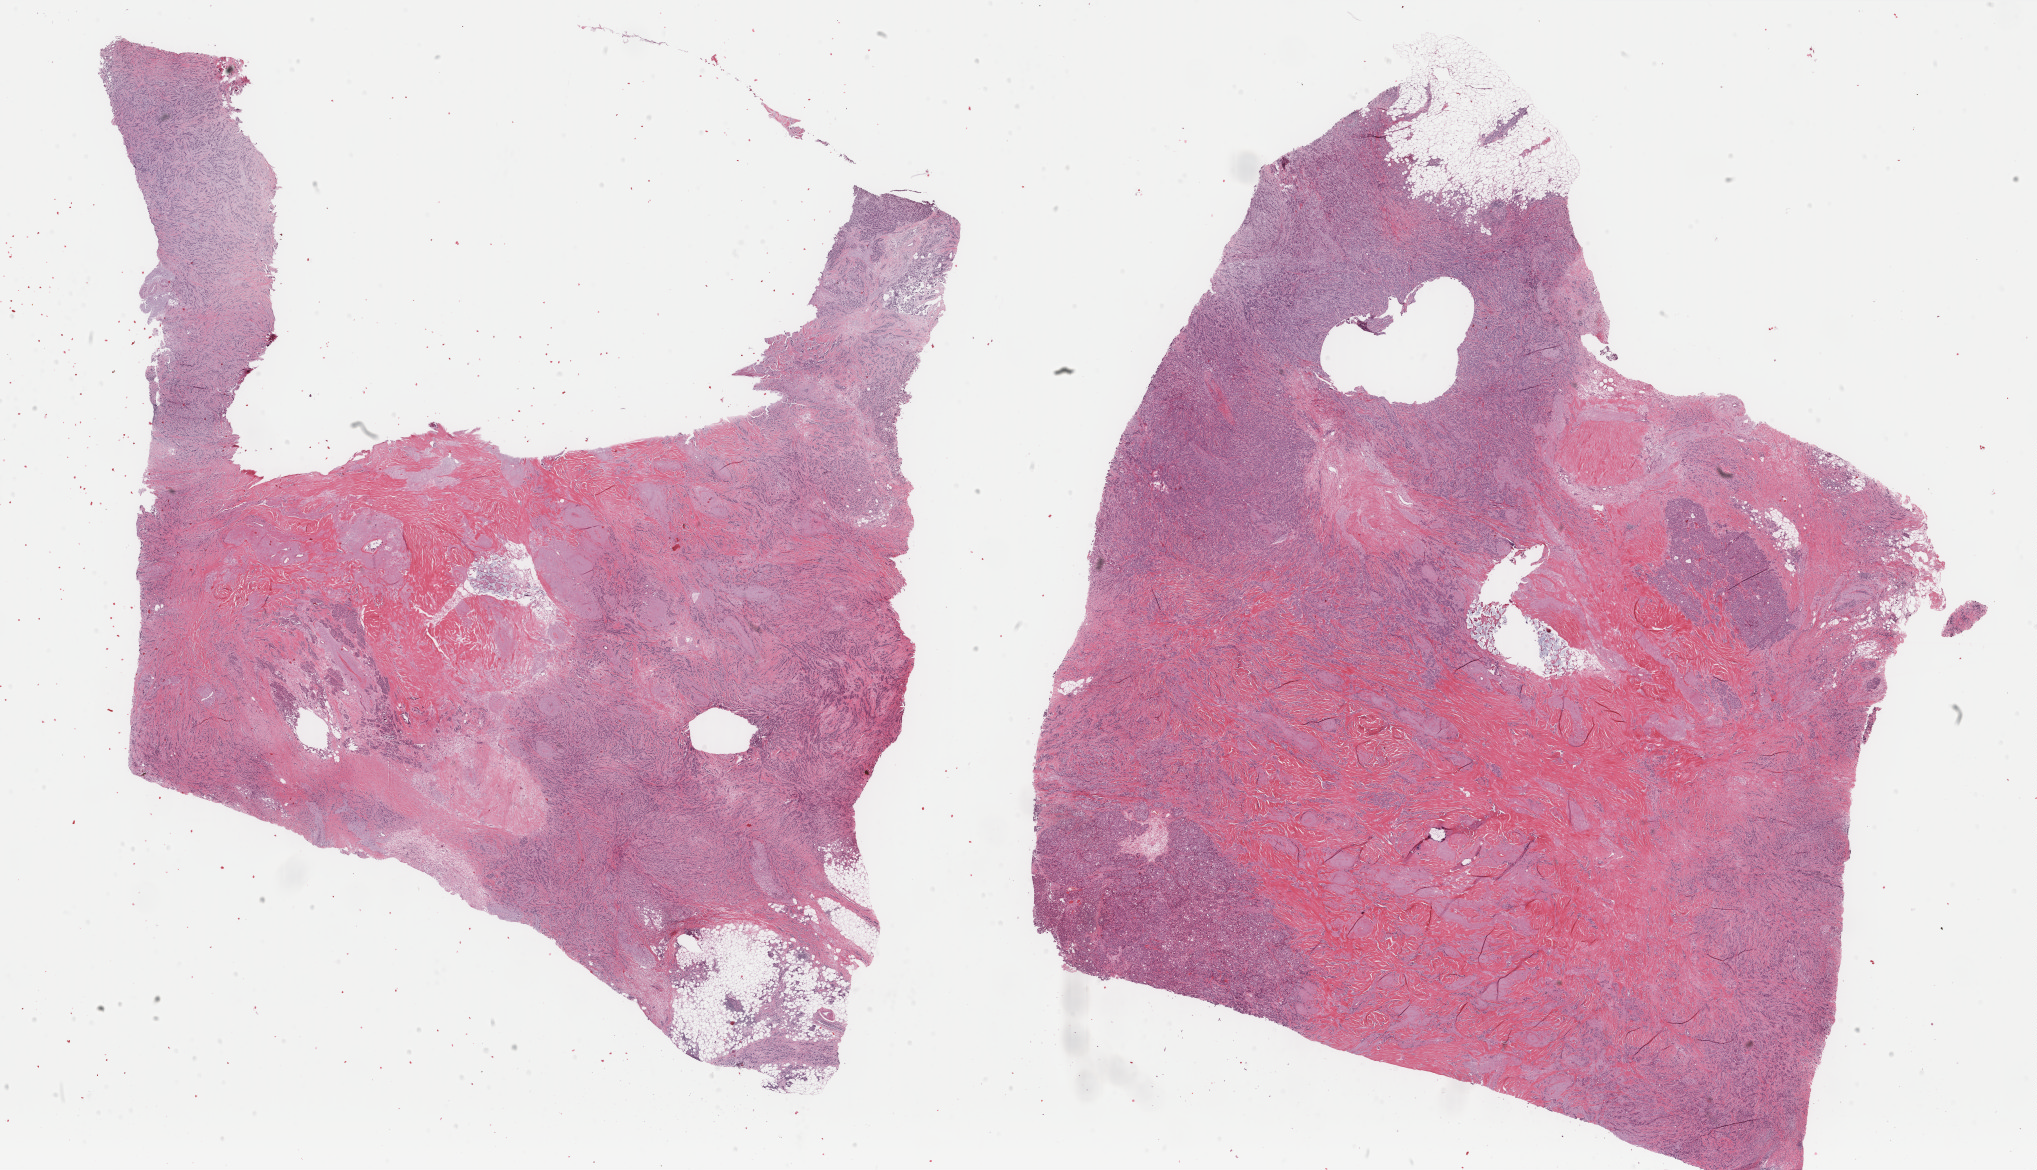
Hematoxylin and eosin (H&E) stained whole-slide image, shown as a low-resolution overview of the whole scanned area (about 32.3 x 18.6 mm), FFPE section, breast, primary tumour sample. Patient: female, age at initial diagnosis 70 years.
AJCC pathologic stage: IIB (6th edition). Histologic diagnosis: Lobular carcinoma, NOS.